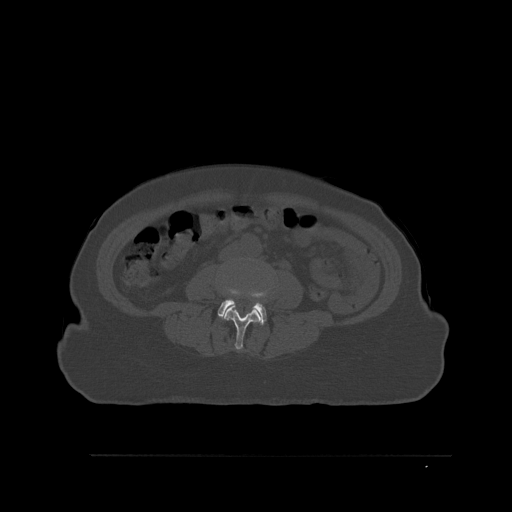
CT including the spine, one axial slice; position 217 of 527 along the scan axis; bone window (W 1800 / L 400 HU); 1.5 mm slice thickness; 512 × 512 image matrix, field of view 470 × 470 mm. Patient: female, 73 years. Case-level facts recorded for this patient, not image findings: primary cancer: breast; vertebrae with lytic lesions (as recorded): L2.
Annotated regions visible in this slice (semi-automatically segmented with operator editing):
- L3 vertebra: bounding box <223,304,262,350> (left, top, right, bottom; pixels)
- L4 vertebra: <217,290,267,325>